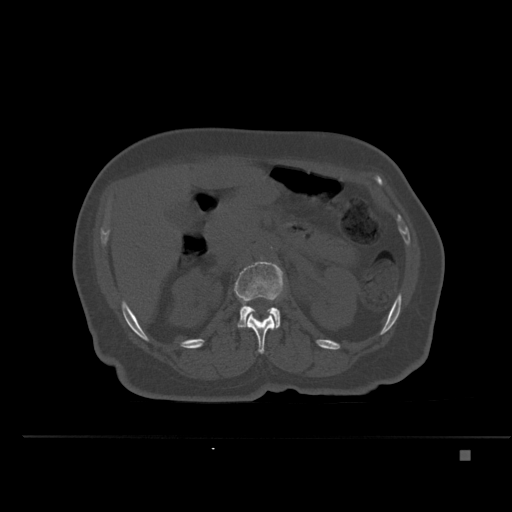
CT including the spine, one axial slice. Position 227 of 477 along the scan axis. Bone window (W 1800 / L 400 HU). 1.5 mm slice thickness. 512 × 512 image matrix, field of view 422 × 422 mm. Patient: female, 74 years. From the clinical record (not read from this slice): primary cancer: colon.
Outlined on this slice (semi-automatically segmented with operator editing):
- L1 vertebra: bounding box (x1, y1, x2, y2) in pixels: (246, 314, 276, 354)
- L2 vertebra: (234, 261, 283, 328)